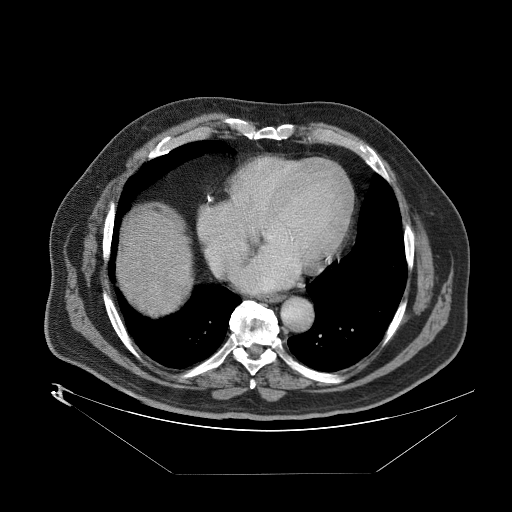
Contrast-enhanced abdominal CT (liver protocol), one axial slice; slice 82 of 89 in the series (ordered by position); one of 2 acquisitions stored at this slice position; soft-tissue window (W 400 / L 40 HU); 512 × 512 image matrix. Case-level facts recorded for this patient, not image findings: diagnosis: hepatocellular carcinoma (patient treated with transarterial chemoembolisation; whether this scan precedes or follows treatment is not stated here); TNM stage (as recorded): Stage-II.
Outlined on this slice (semi-automatic segmentation, software-assisted and operator-edited):
- abdominal aorta: bounding box [x1, y1, x2, y2] px = [277, 296, 312, 330]
- liver parenchyma outside the tumour (the mass and vessels are separate outlines, so this box may not span the whole liver): [122, 210, 180, 292]
- liver vessels: [172, 243, 174, 245]